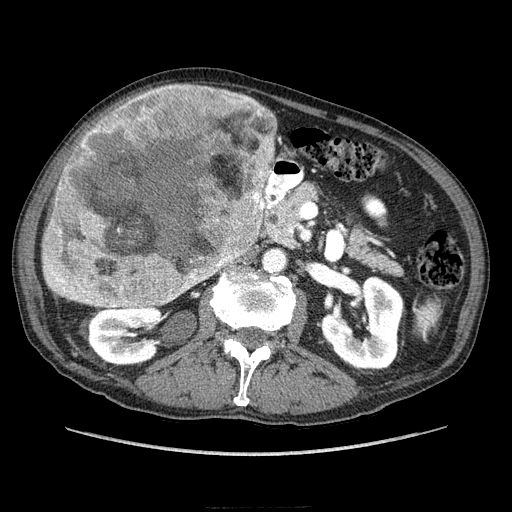
Contrast-enhanced abdominal CT (liver protocol), one axial slice. Position 107 of 218 along the scan axis. Reconstruction kernel STANDARD. 100 kVp. Soft-tissue window (W 400 / L 40 HU). 2.5 mm slice thickness. 512 × 512 image matrix, field of view 380 × 380 mm. Case-level facts recorded for this patient, not image findings: diagnosis: hepatocellular carcinoma (patient treated with transarterial chemoembolisation; whether this scan precedes or follows treatment is not stated here); TNM stage (as recorded): Stage-IIIA; Child-Pugh class: A; tumour differentiation: well differentiated; tumour nodularity: multinodular.
Outlined on this slice (semi-automatically segmented with operator editing):
- liver parenchyma outside the tumour (the mass and vessels are separate outlines, so this box may not span the whole liver): bounding box (x1, y1, x2, y2) in pixels: (229, 156, 273, 262)
- mass: (40, 83, 277, 311)